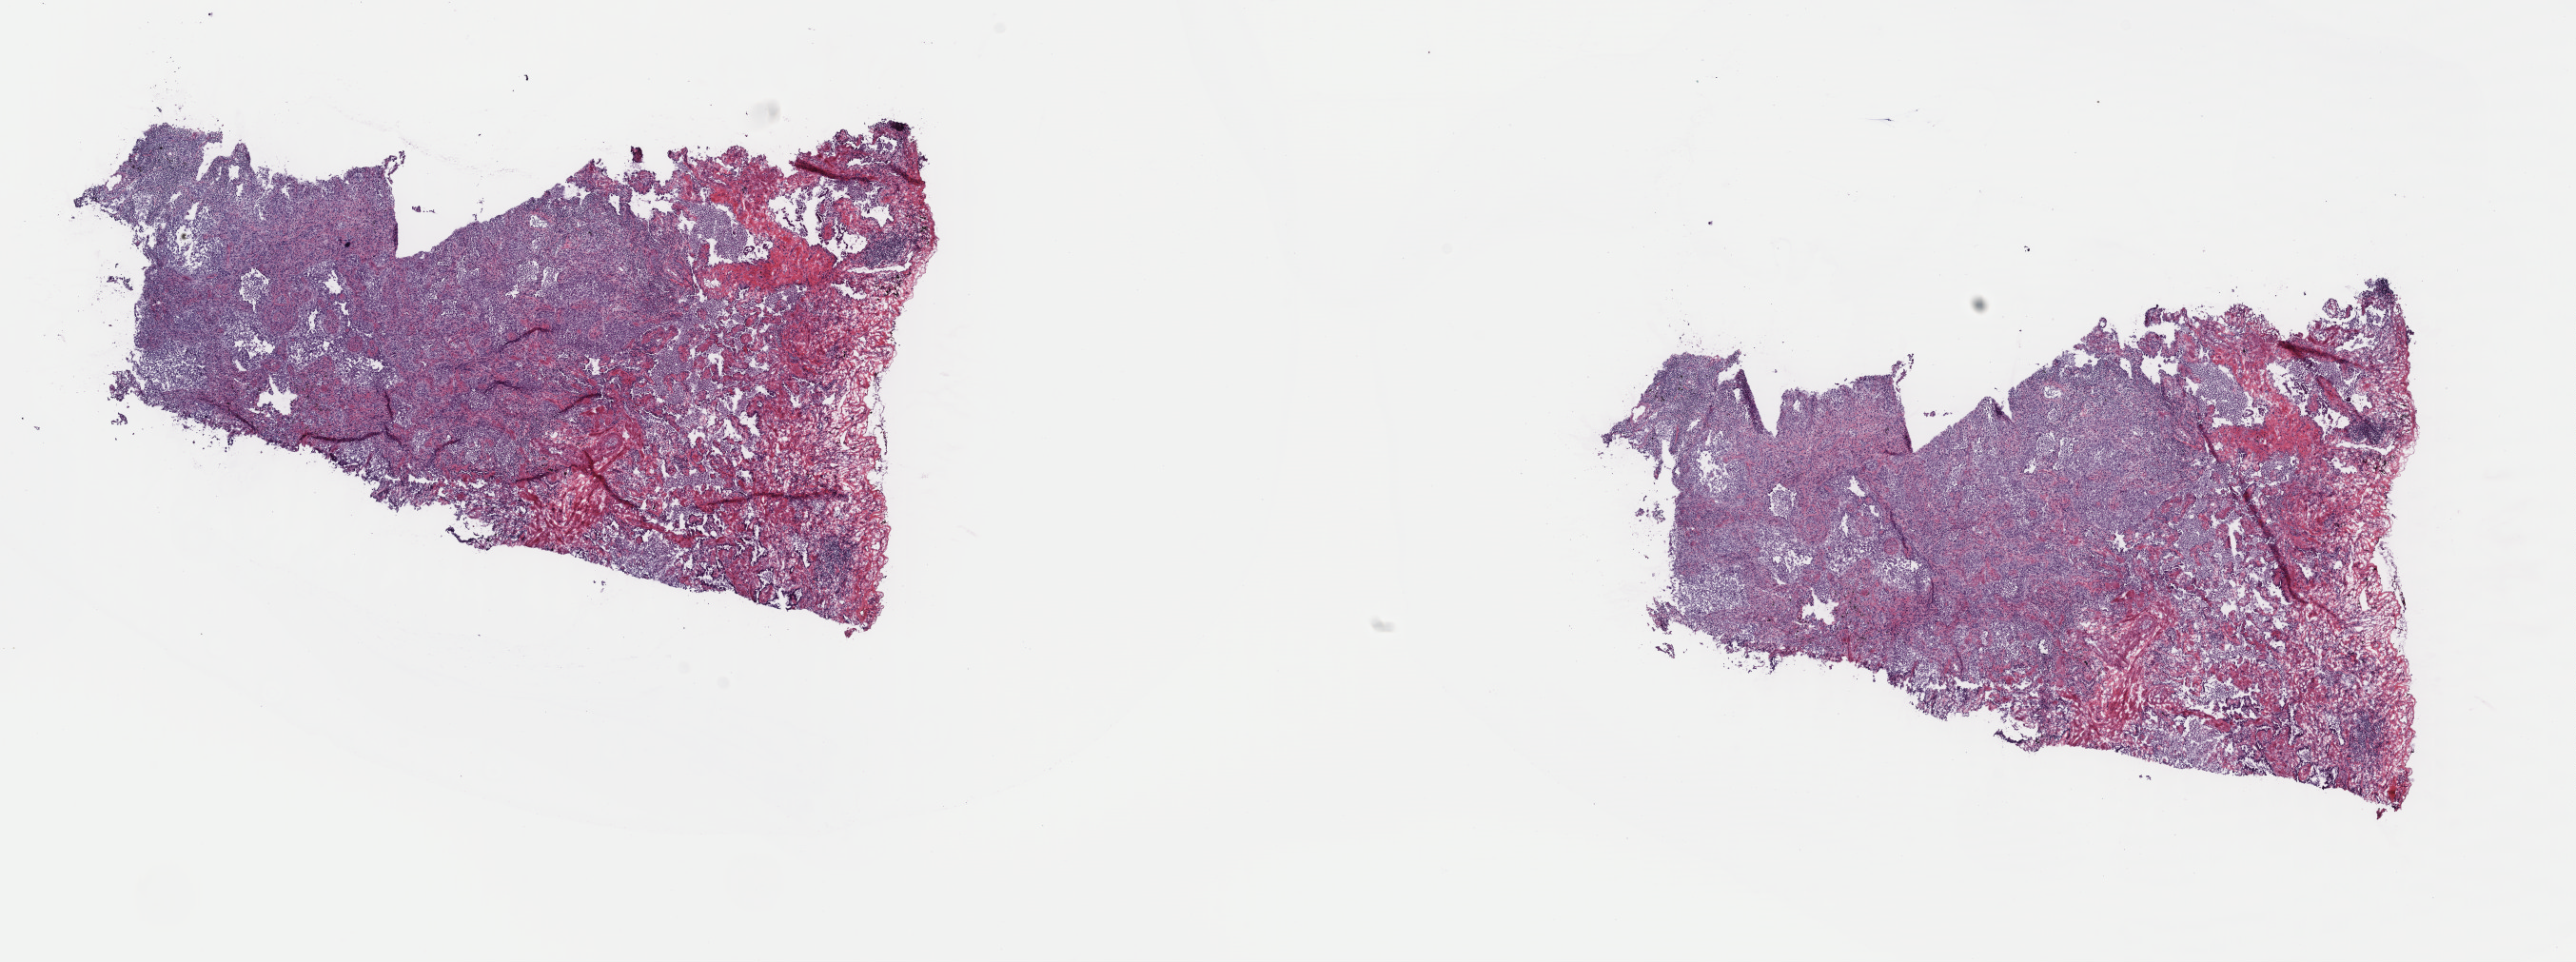
H&E whole-slide image, shown as a low-resolution overview of the whole scanned area (about 21.4 x 8.0 mm, from a 40x scan), frozen section, lung, primary tumour sample. Male patient; age at initial diagnosis 72 years. Composition of this section per pathologist review: tumour cells 92%, tumour nuclei 60%, normal cells 0%, stromal cells 8%, necrosis 0%. Inflammatory infiltration, as recorded: lymphocyte infiltration 0%, monocyte infiltration 0%, neutrophil infiltration 0%.
AJCC pathologic stage: IIA. Pathologic diagnosis: Adenocarcinoma, NOS (lower lobe, lung).